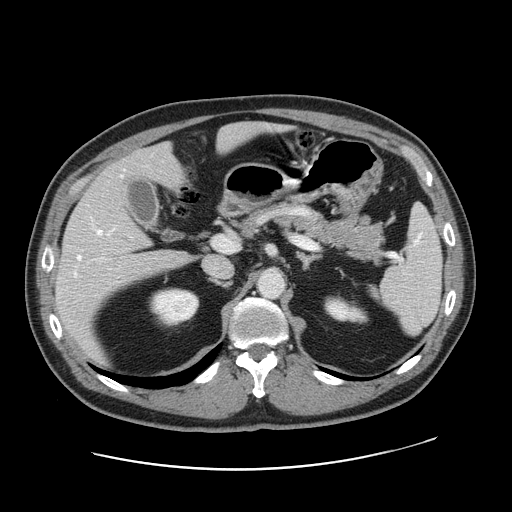
Contrast-enhanced abdominal CT, one axial slice; slice 96 of 178 in the series (ordered by position); 120 kVp; intravenous contrast given; soft-tissue window (W 400 / L 40 HU); 512 × 512 image matrix, field of view 403 × 403 mm. Male patient, age 63 years. Case-level facts recorded for this patient, not image findings: diagnosis: colorectal cancer liver metastases, imaged before liver resection; multiple liver metastases: yes; largest metastasis: 8 cm.
Structures marked on this image (manually delineated by an expert):
- hepatic veins: bounding box (x1, y1, x2, y2) in pixels: (74, 175, 122, 274)
- liver: (56, 123, 274, 356)
- planned liver remnant (the part of the liver to remain after resection): (118, 123, 275, 189)
- portal vein (with intrahepatic branches): (99, 236, 236, 260)